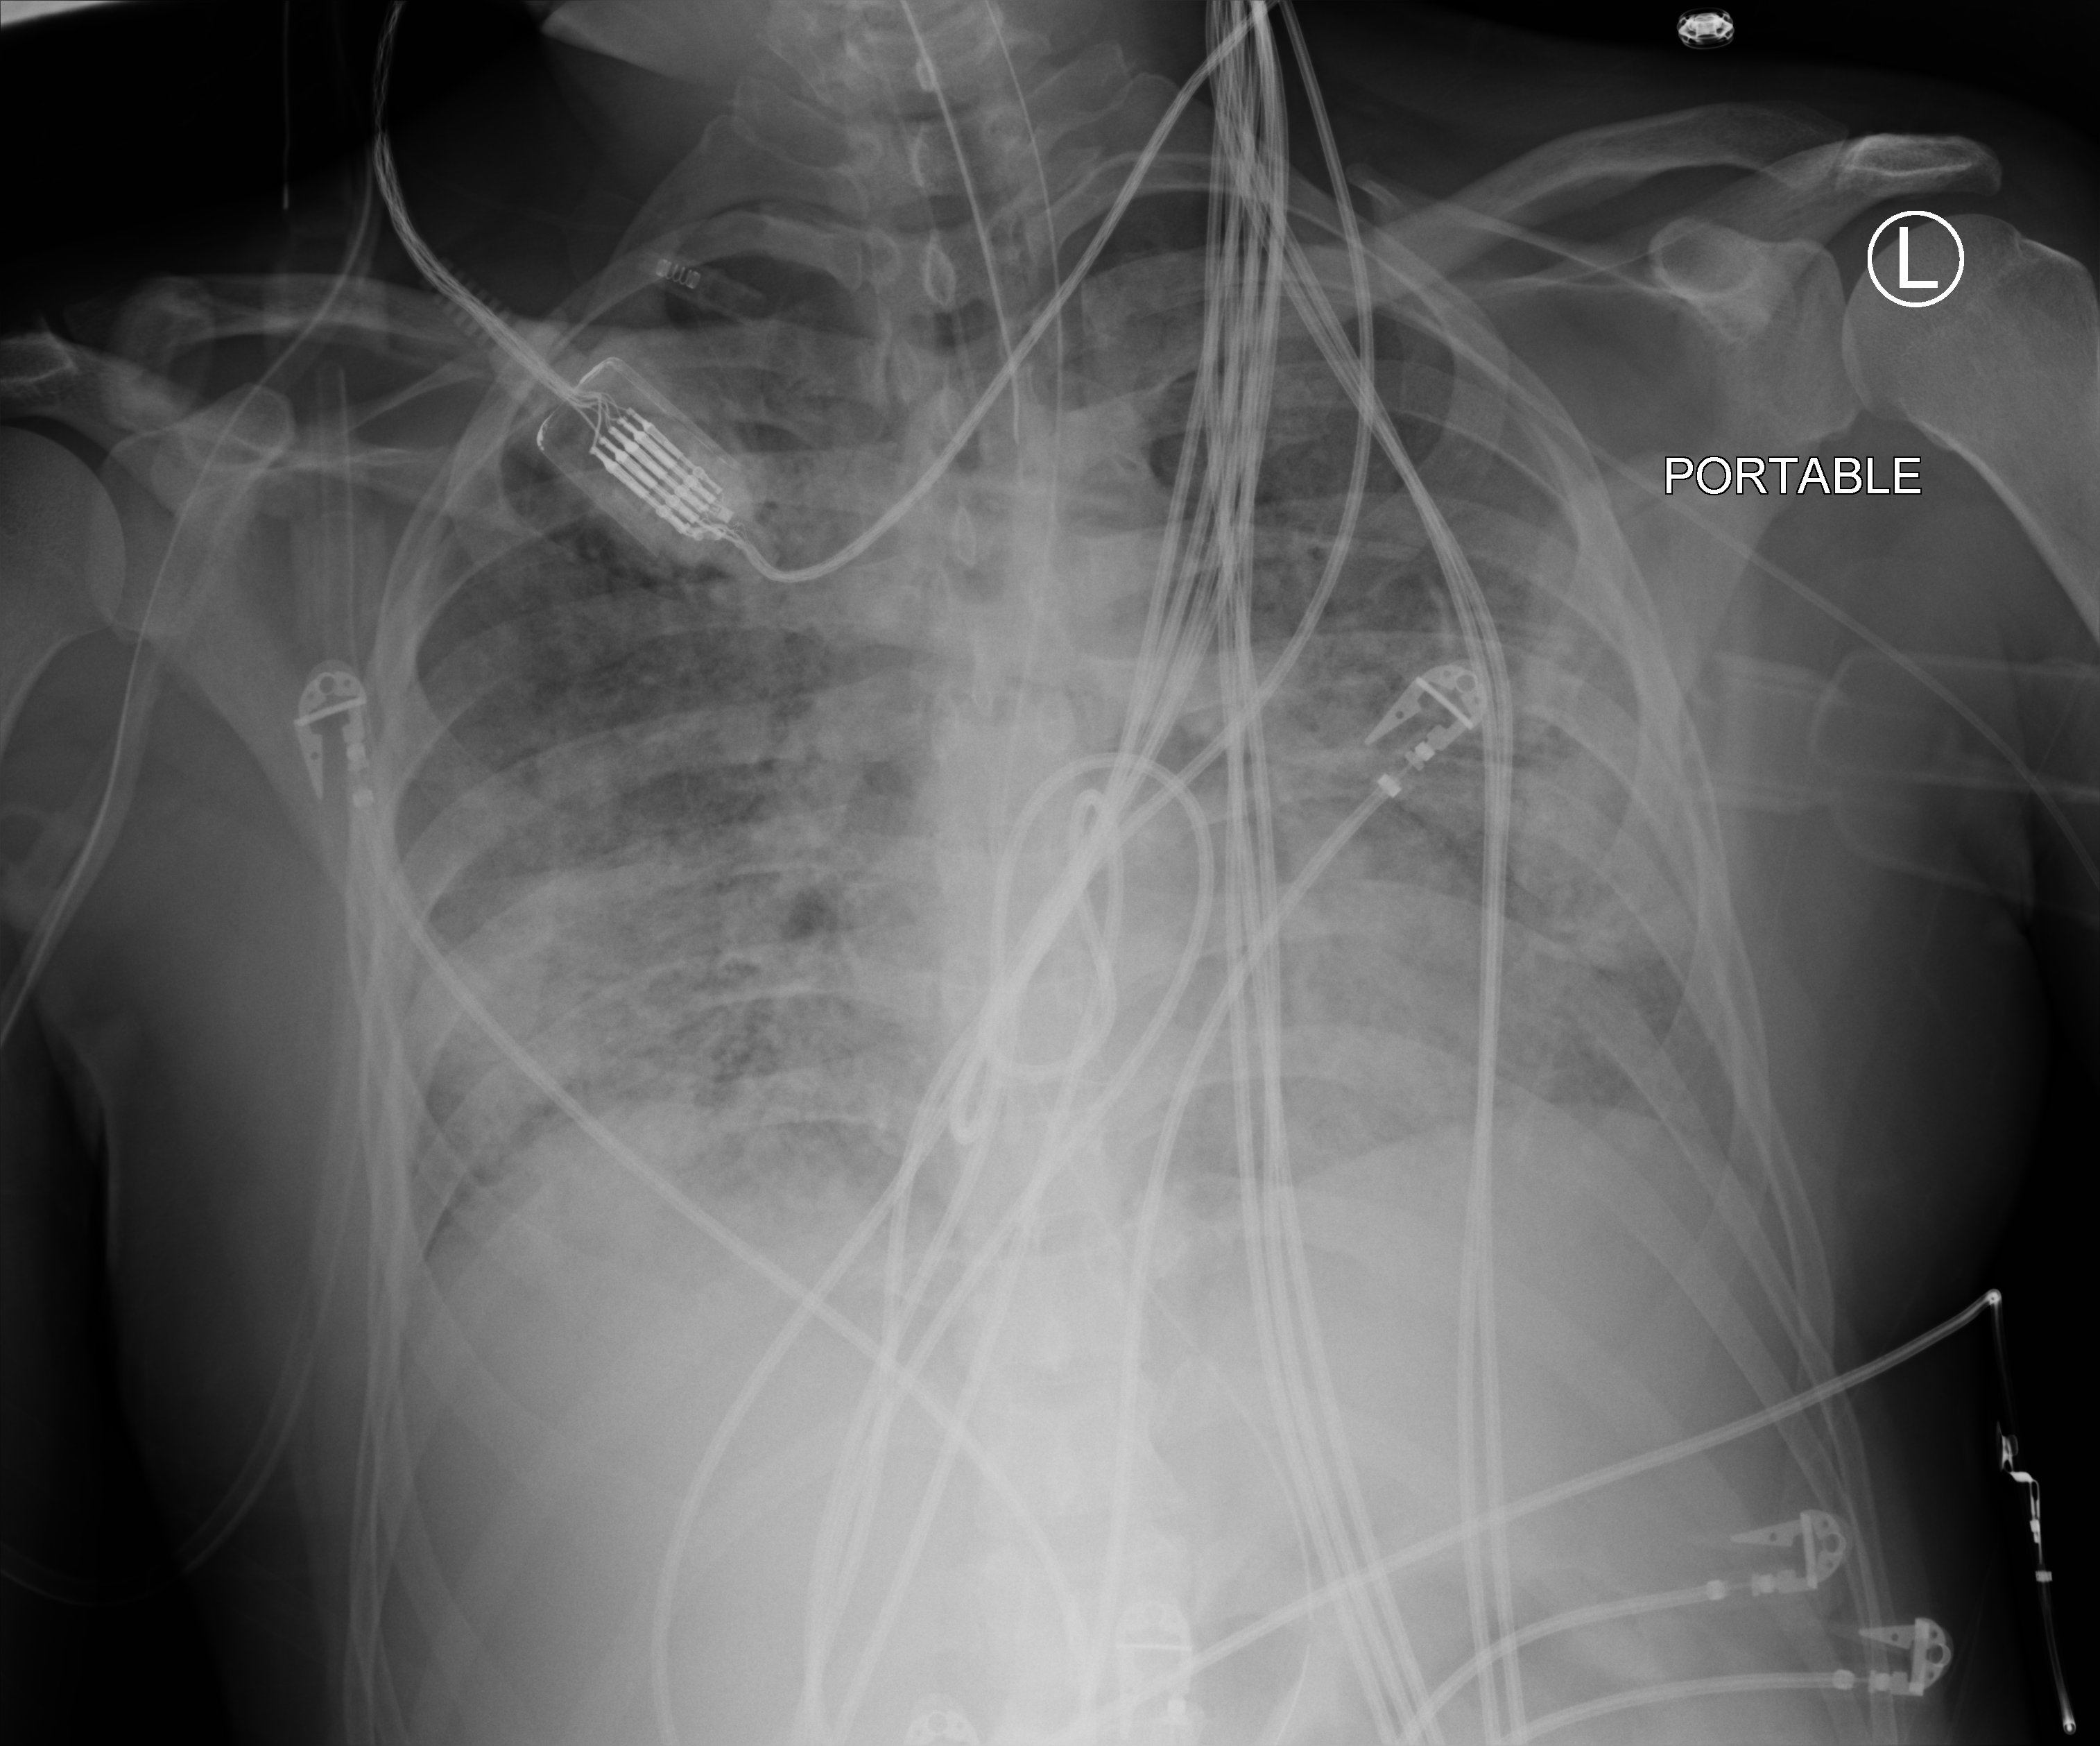
Portable chest radiograph. Male patient hospitalised with COVID-19, age 18–59 years.
Hospital-stay facts (about this admission, not read from this image; timing relative to this image not recorded):
- COPD (admission record): no
- mechanically ventilated during this hospital stay: yes
- diabetes (admission record): no